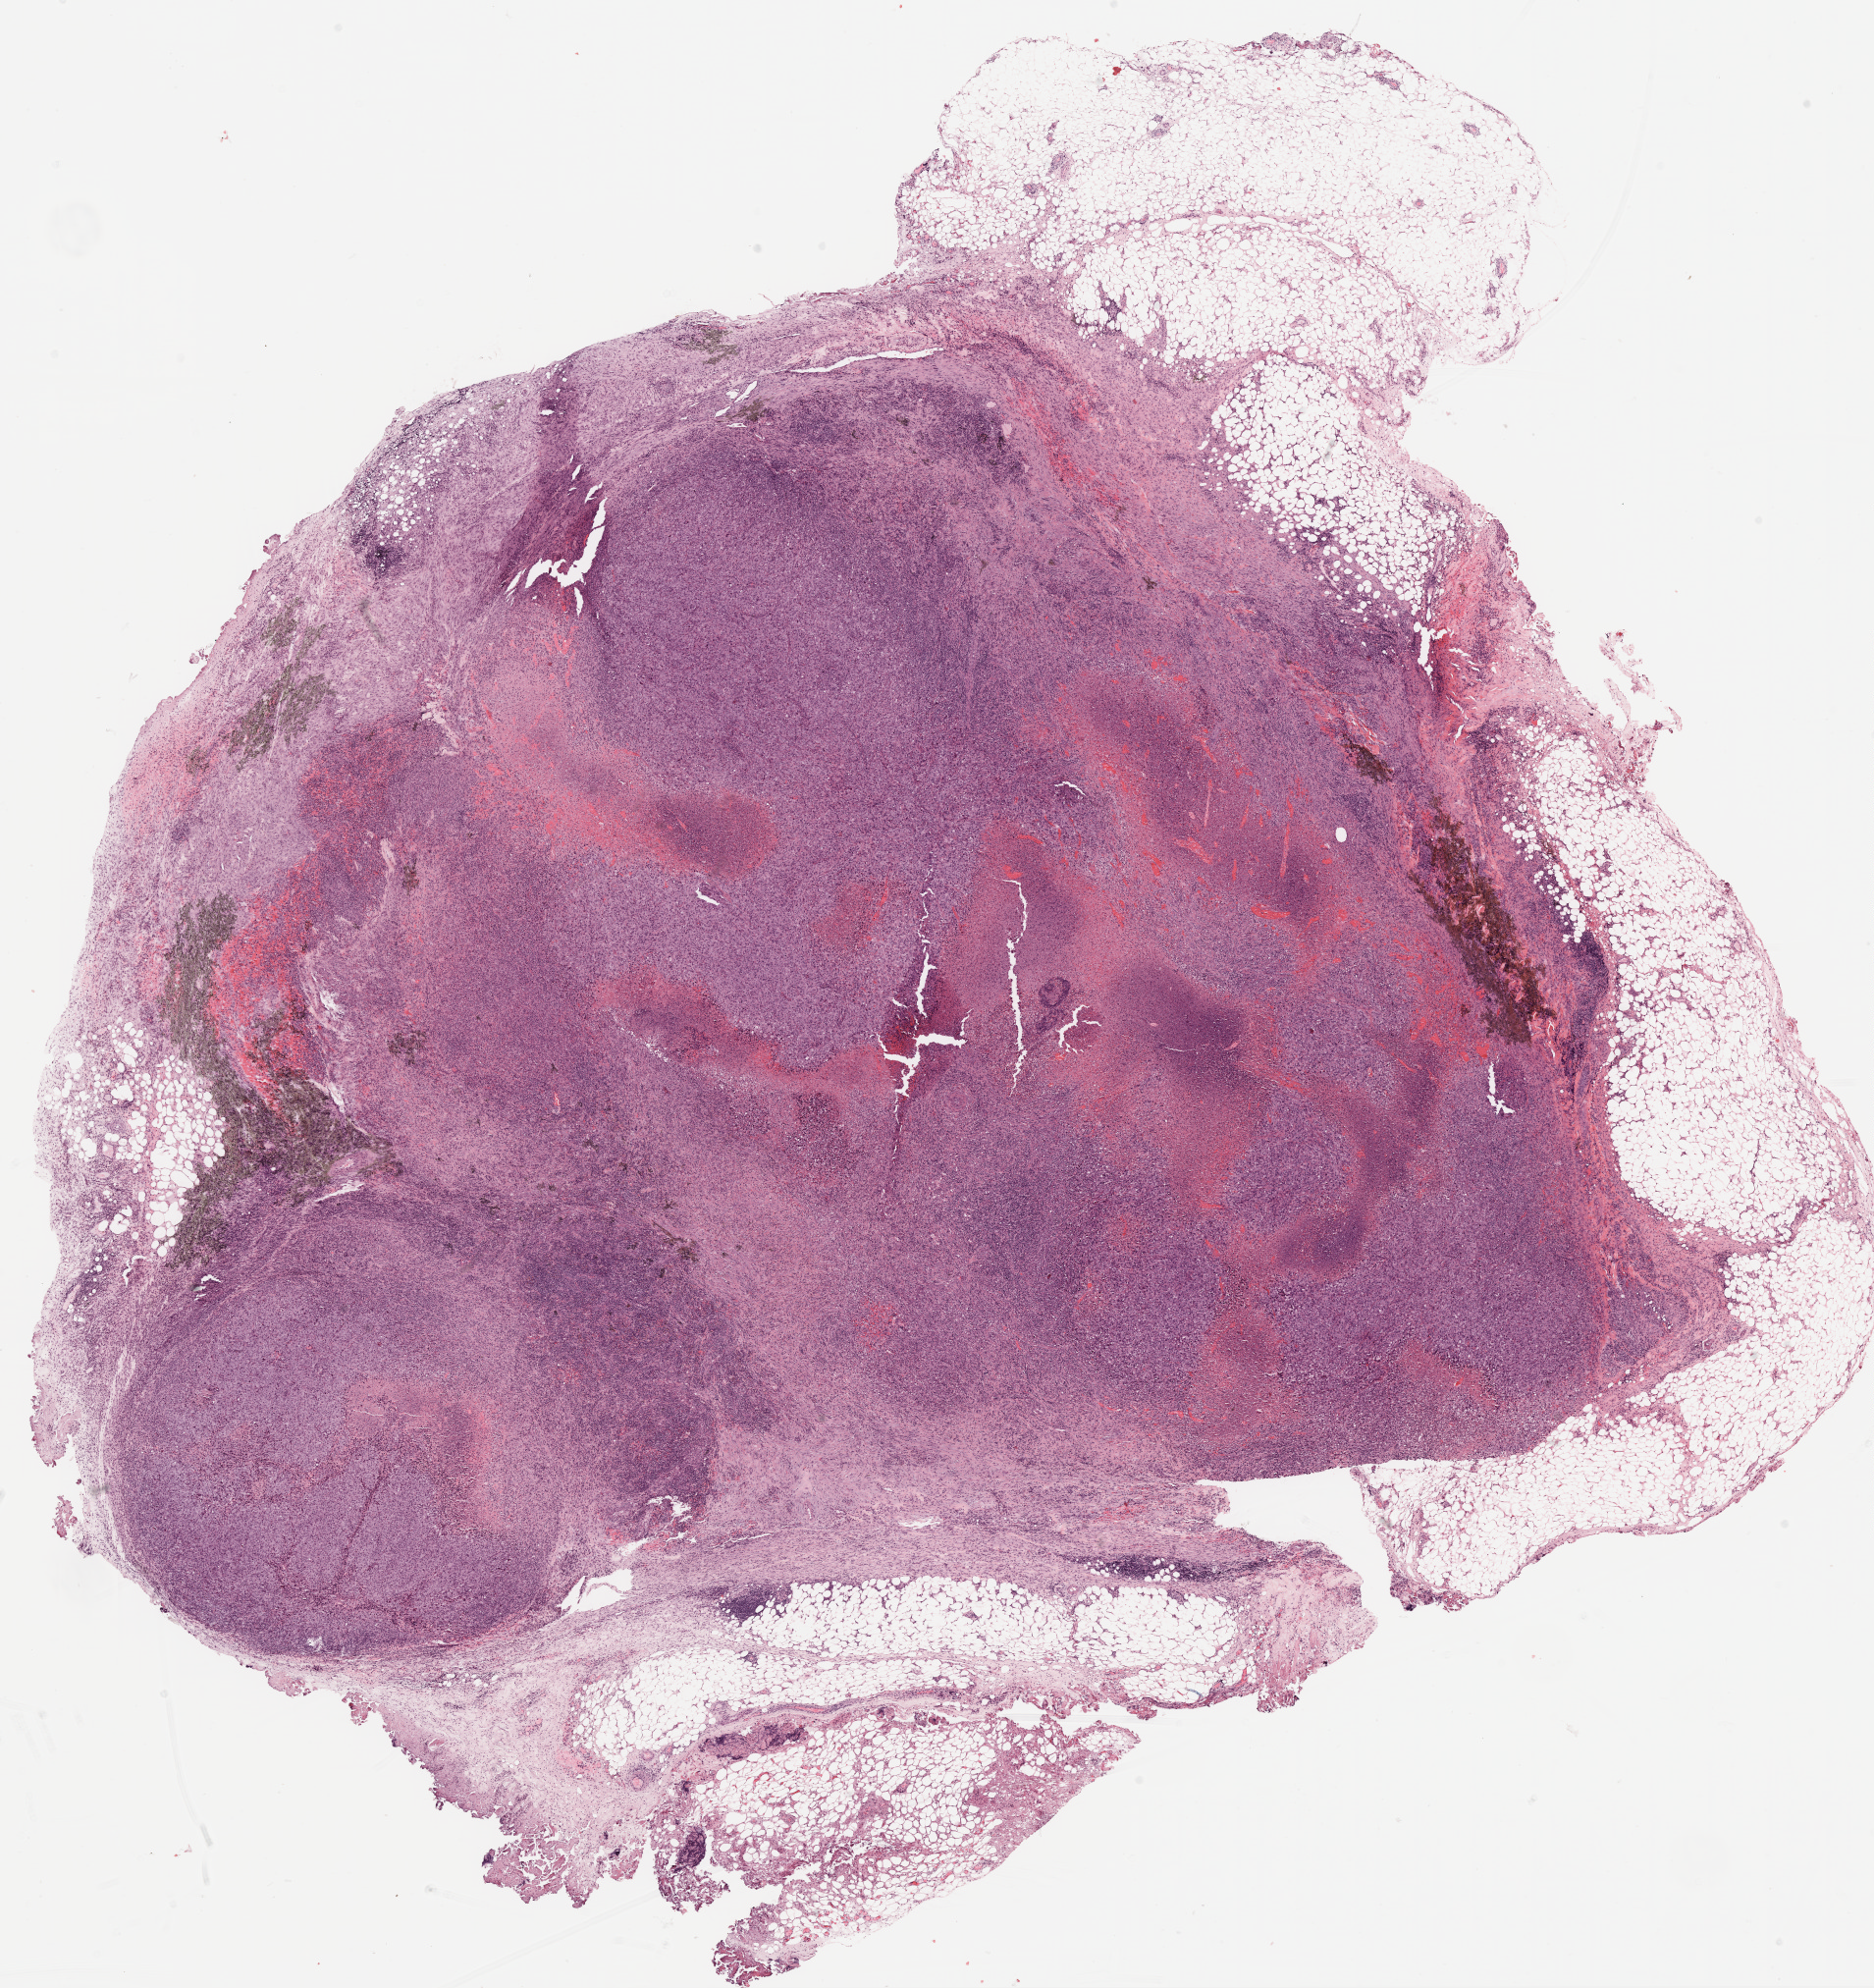
Whole-slide histology image, Hematoxylin and eosin (H&E) stained, low-resolution overview of the scanned area, about 15.4 x 16.3 mm; formalin-fixed paraffin-embedded (FFPE) diagnostic section; metastatic tumour sample, sampled site not recorded. Patient: male, age at initial diagnosis 48 years.
This section: metastatic tumour tissue. Patient diagnosis: Malignant melanoma, NOS.